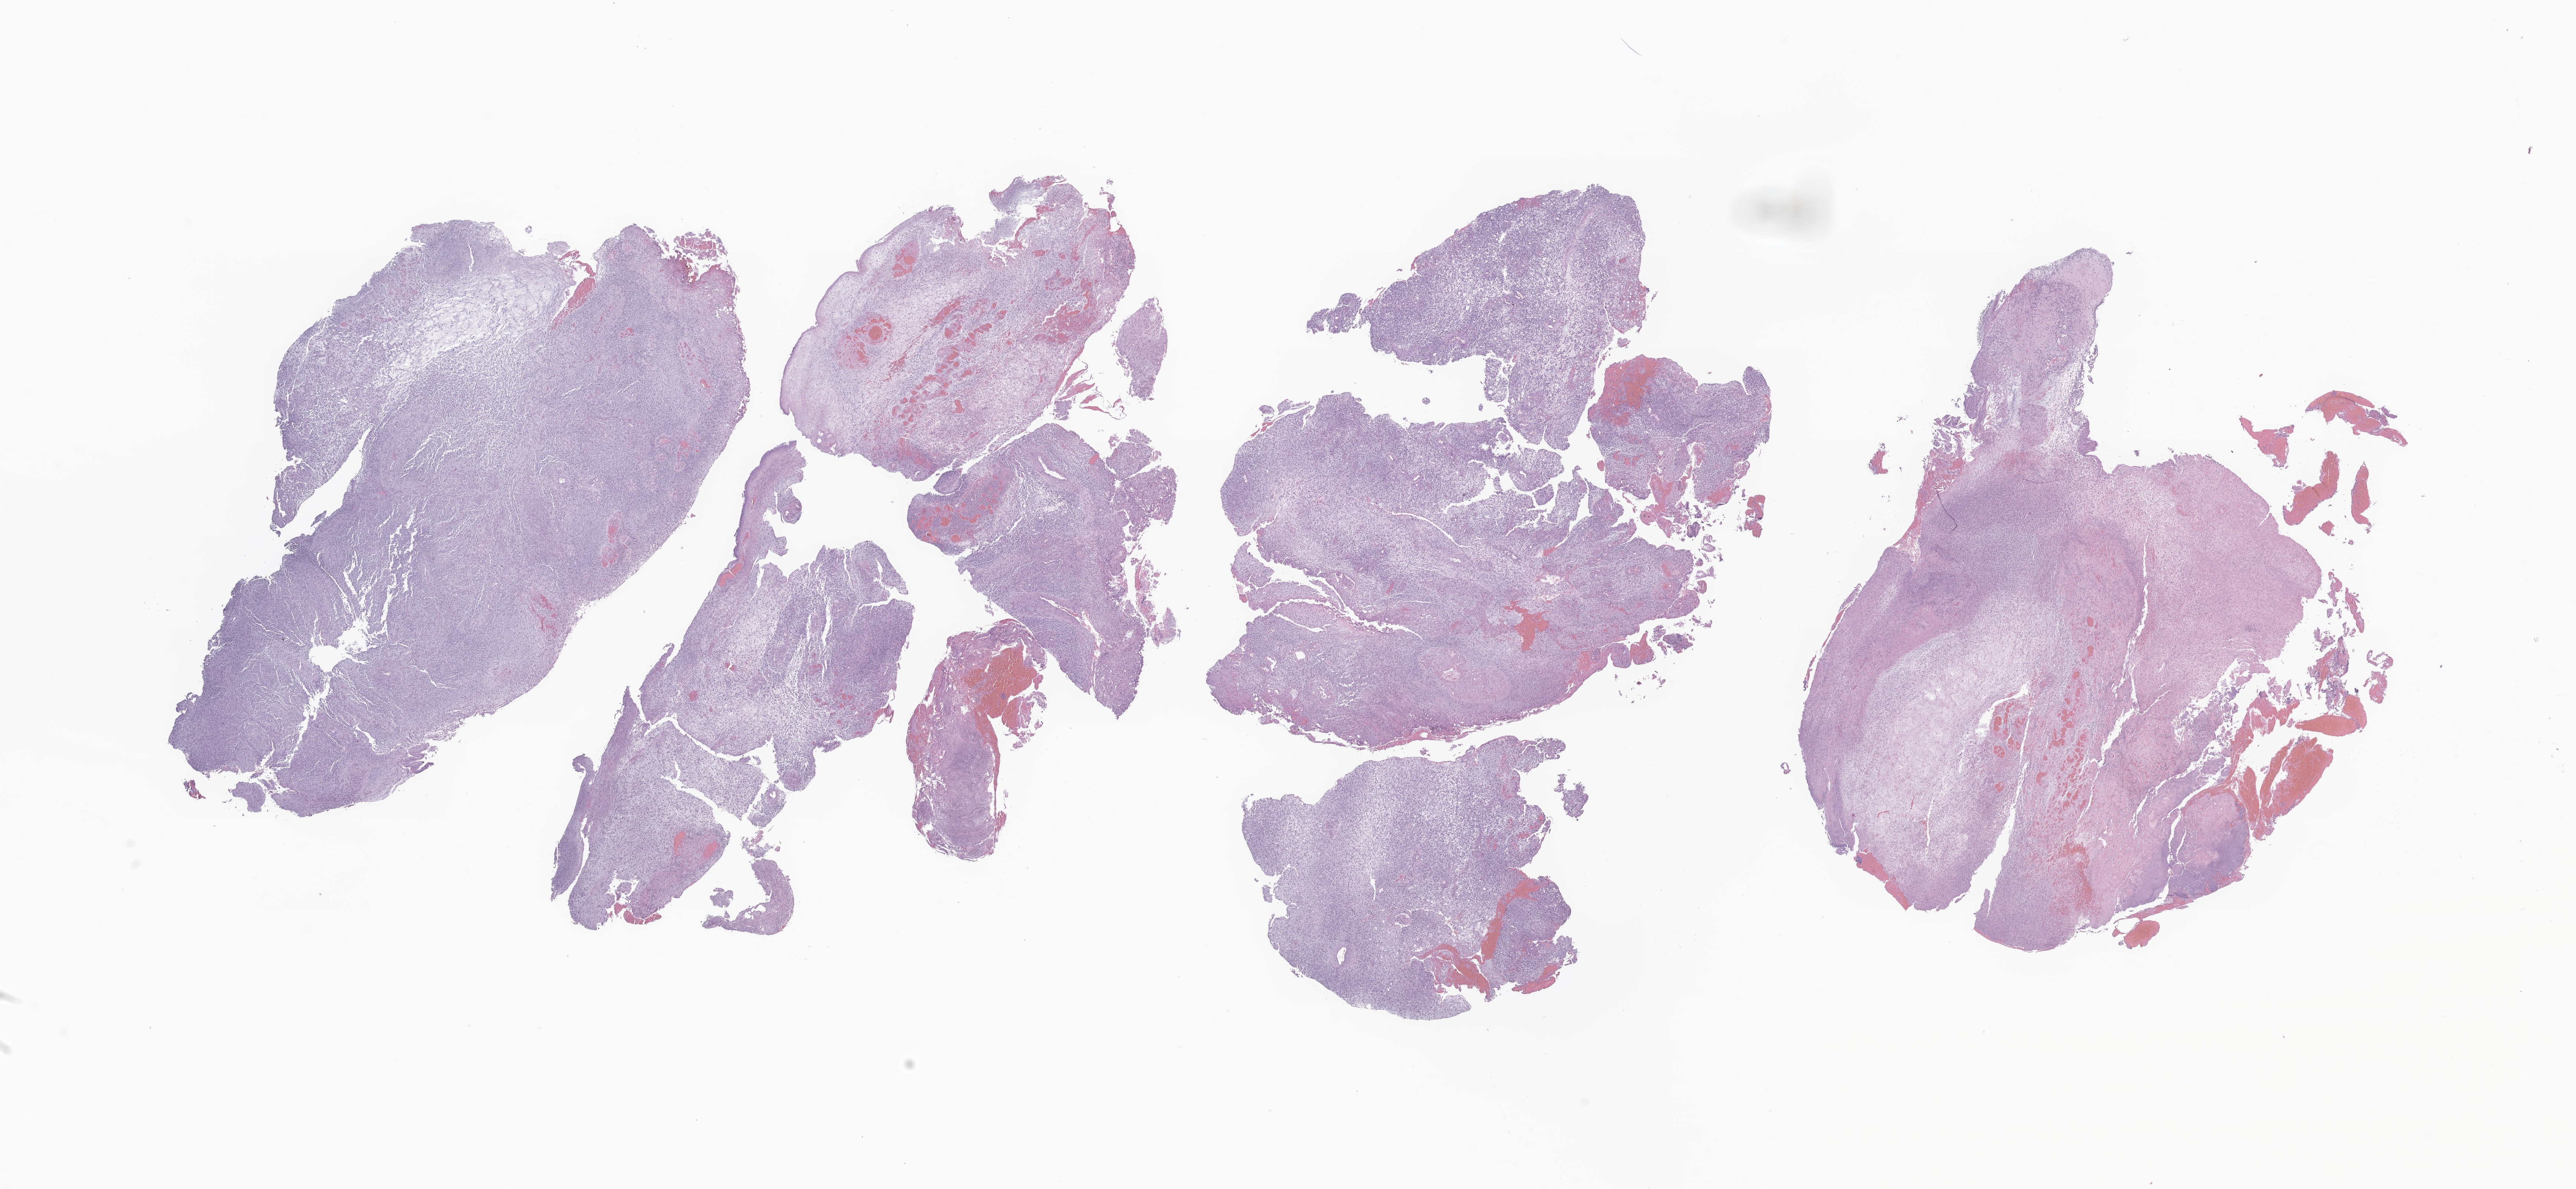
Haematoxylin and eosin whole-slide image of tumor tissue from the nasal cavity, a low-resolution overview of the entire scanned area, about 29.3 x 13.5 mm; formalin-fixed paraffin-embedded section. Female patient, age 143 months.
- diagnosis (ICD-O-3 morphology term): Neoplasm, malignant